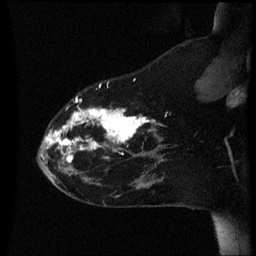
Breast MRI (dynamic contrast-enhanced), one sagittal slice; position 15 of 60 along the scan axis; dynamic contrast-enhanced series, image 2 of 3 at this slice position (ordered by acquisition); 1.5 T; TE 4.2 ms, TR 8.4 ms; 2.2 mm slice thickness; 256 × 256 image matrix, field of view 200 × 200 mm. Patient: female, 35 years. From the clinical record (not read from this slice): setting: breast cancer imaged before/during neoadjuvant chemotherapy; receptor status: HER2-positive.
Outlined on this slice (semi-automatic segmentation, software-assisted and operator-edited):
- analysis volume of interest (the breast-tissue region the enhancement analysis was run in; not a lesion): box from (x=39, y=72) to (x=168, y=173) px
- tumour enhancement mask (voxels above the 70 % enhancement threshold inside the analysis volume of interest): (x=45, y=84)–(x=165, y=163)